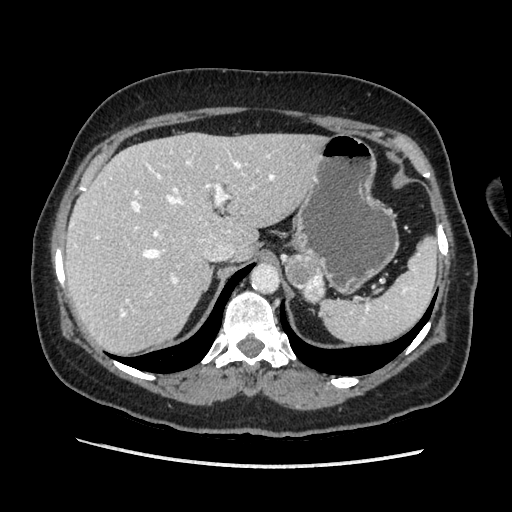
Contrast-enhanced abdominal CT, one axial slice; position 144 of 203 along the scan axis; soft-tissue window (W 400 / L 40 HU); 1.25 mm slice thickness; 512 × 512 image matrix. Female patient. Case-level facts recorded for this patient, not image findings: diagnosis: adrenocortical carcinoma; tumour side: left adrenal; tumour size at pathology: 6.5 cm; Ki-67 index: 22 %.
Structures marked on this image (semi-automatically segmented with operator editing):
- mass: bounding box <285,256,323,303> (left, top, right, bottom; pixels)